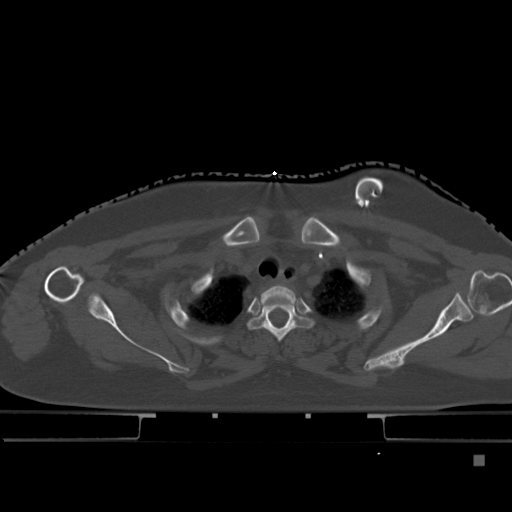
CT including the spine, one axial slice; slice 361 of 495 in the series (ordered by position); bone window (W 1800 / L 400 HU); 512 × 512 image matrix, field of view 404 × 404 mm. Patient: female, 33 years. Case-level facts recorded for this patient, not image findings: primary cancer: breast; vertebrae with lytic lesions (as recorded): T1.
Structures marked on this image (semi-automatic segmentation, software-assisted and operator-edited):
- T1 vertebra: bounding box (x1, y1, x2, y2) in pixels: (261, 285, 296, 304)
- T2 vertebra: (248, 301, 312, 342)